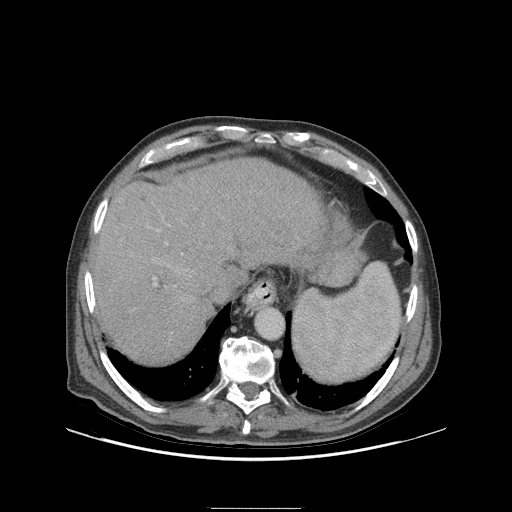
Contrast-enhanced abdominal CT (liver protocol), one axial slice; position 79 of 105 along the scan axis; reconstruction kernel STANDARD; soft-tissue window (W 400 / L 40 HU); 2.5 mm slice thickness; 512 × 512 image matrix, field of view 440 × 440 mm. From the clinical record (not read from this slice): diagnosis: hepatocellular carcinoma (patient treated with transarterial chemoembolisation; whether this scan precedes or follows treatment is not stated here); TNM stage (as recorded): Stage-I; Child-Pugh class: A; tumour nodularity: uninodular; tumour size: 5.1 cm.
Annotated regions visible in this slice (semi-automatically segmented with operator editing):
- abdominal aorta: bounding box [x1, y1, x2, y2] px = [255, 309, 283, 338]
- liver parenchyma outside the tumour (the mass and vessels are separate outlines, so this box may not span the whole liver): [94, 158, 324, 362]
- liver vessels: [153, 229, 167, 286]